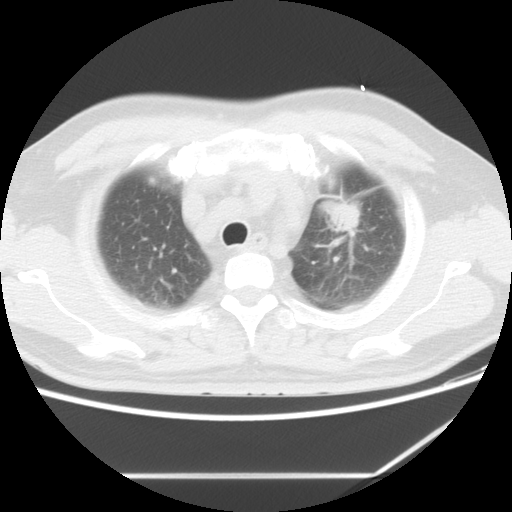
Chest CT, one axial slice; slice 10 of 13 in the series (ordered by position); lung window (W 1500 / L -600 HU); 5 mm slice thickness; 512 × 512 image matrix. Male patient, age 56 years. Case-level facts recorded for this patient, not image findings: clinical TNM (as recorded): T2 N3 M1.
Structures marked on this image (rectangle marked by the reading radiologist):
- lung tumour (recorded histology: adenocarcinoma): bounding box [x1, y1, x2, y2] px = [323, 194, 365, 238]